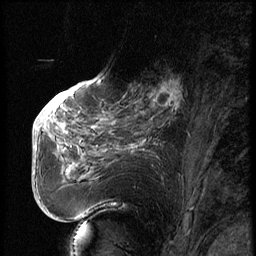
Breast MRI (dynamic contrast-enhanced), one sagittal slice. Slice 30 of 74 in the series (ordered by position). Dynamic contrast-enhanced series, image 2 of 3 at this slice position (ordered by acquisition). 1.5 T. TE 4.2 ms, TR 9 ms. 2.5 mm slice thickness. 256 × 256 image matrix, field of view 180 × 180 mm. Female patient, age 56 years. Case-level facts recorded for this patient, not image findings: setting: breast cancer imaged before/during neoadjuvant chemotherapy.
Annotated regions visible in this slice (semi-automatic segmentation, software-assisted and operator-edited):
- analysis volume of interest (the breast-tissue region the enhancement analysis was run in; not a lesion): box from (x=123, y=71) to (x=195, y=131) px
- tumour enhancement mask (voxels above the 140 % enhancement threshold inside the analysis volume of interest): (x=151, y=78)–(x=182, y=112)